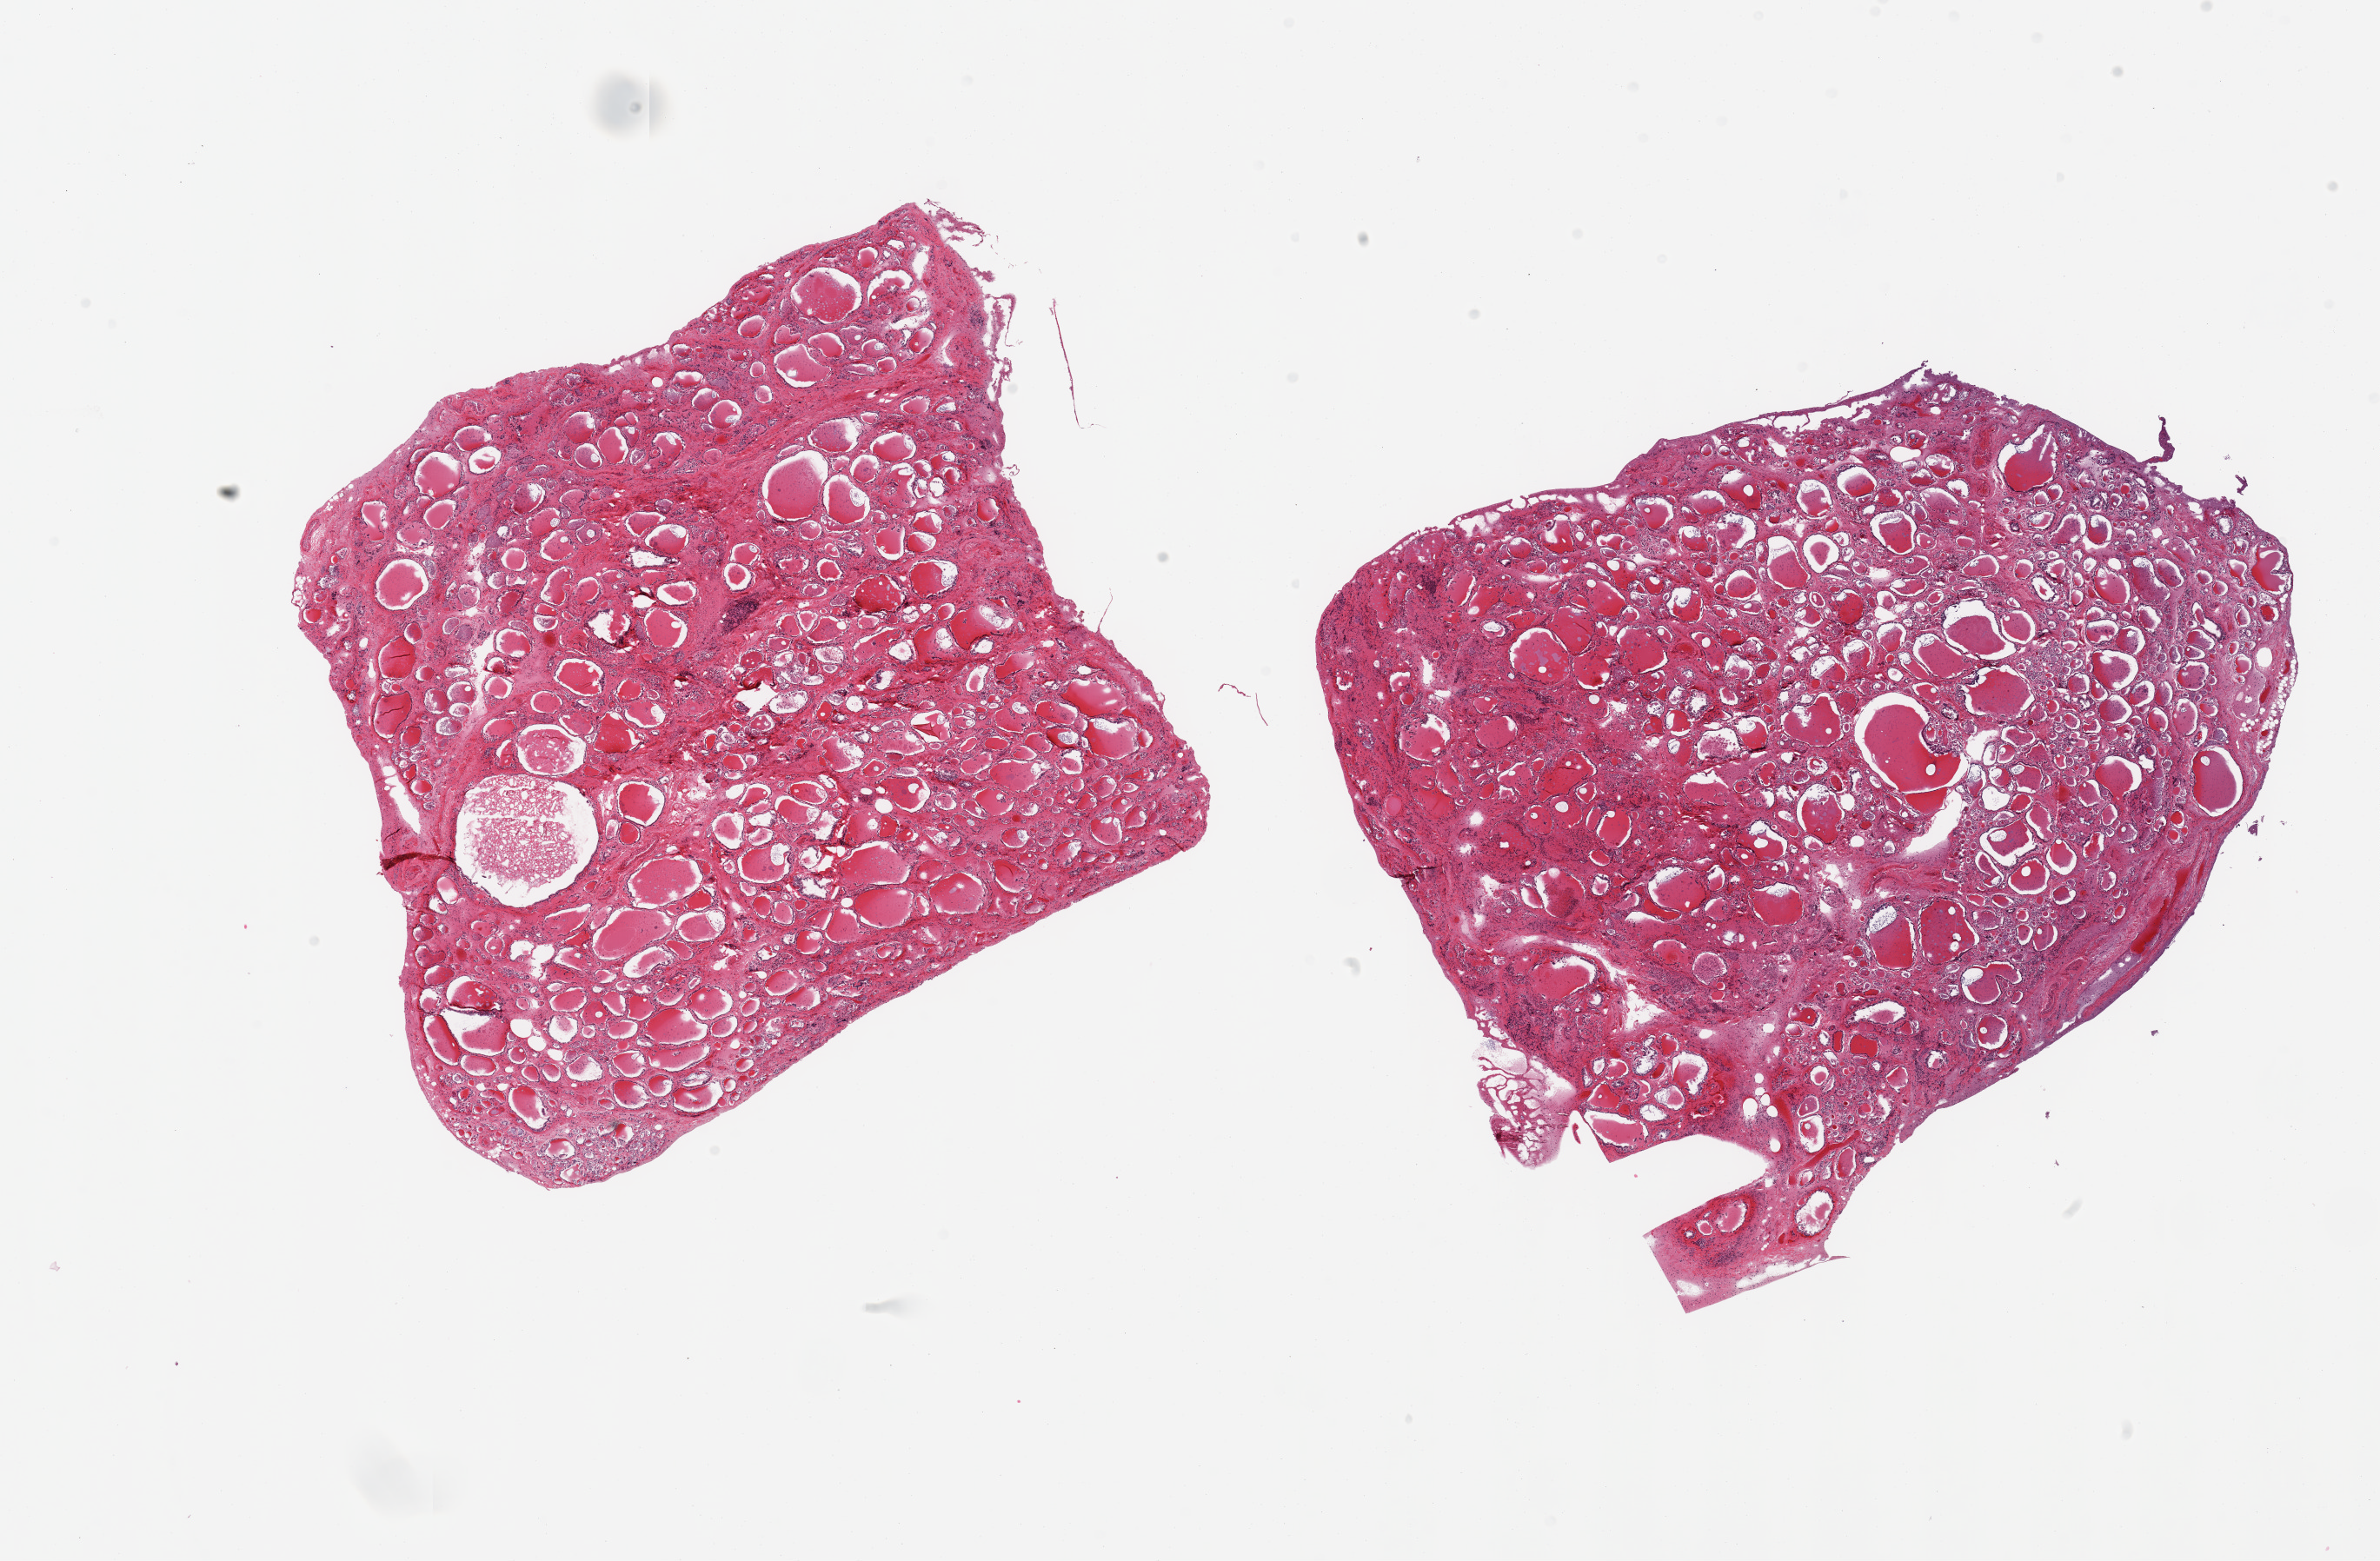
Whole-slide image, haematoxylin and eosin stain, brightfield, shown as a low-resolution overview of the whole scanned area (about 21.7 x 14.2 mm), PAXgene-fixed paraffin-embedded (PFPE) section, sampled site (target tissue): thyroid, tissue donor sample. Donor: female.
Pathologist's review note for this sample: 2 pieces, few colloid cysts.